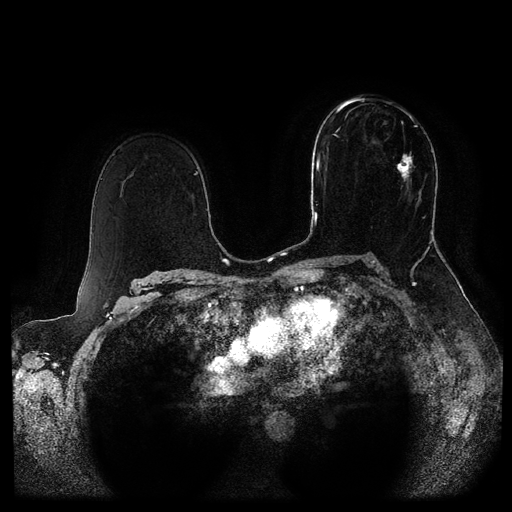
Breast MRI (dynamic contrast-enhanced, multi-phase), one axial slice; slice 59 of 116 in the series (ordered by position); dynamic contrast-enhanced series, time point 2 of 5 at this slice position (early post-contrast); 1.5 T; TE 2.6 ms, TR 5.3 ms; 512 × 512 image matrix, field of view 370 × 370 mm. Patient: female, 51 years.
Structures marked on this image (semi-automatic segmentation, software-assisted and operator-edited):
- breast lesion (labelled 'tumour' in the annotation; benign lesions carry a separate 'benign' label): box from (x=373, y=120) to (x=414, y=187) px